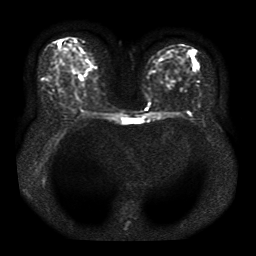
Breast MRI, one axial slice; position 17 of 41 along the scan axis; diffusion-weighted series; image 2 of 4 stored at this slice position (different b-values; order by instance number); 1.5 T; 5 mm slice thickness; 256 × 256 image matrix, field of view 330 × 330 mm. Female patient.
Structures marked on this image (outlined manually by an expert reader):
- tumour on diffusion-weighted imaging: bounding box <72,58,84,70> (left, top, right, bottom; pixels)